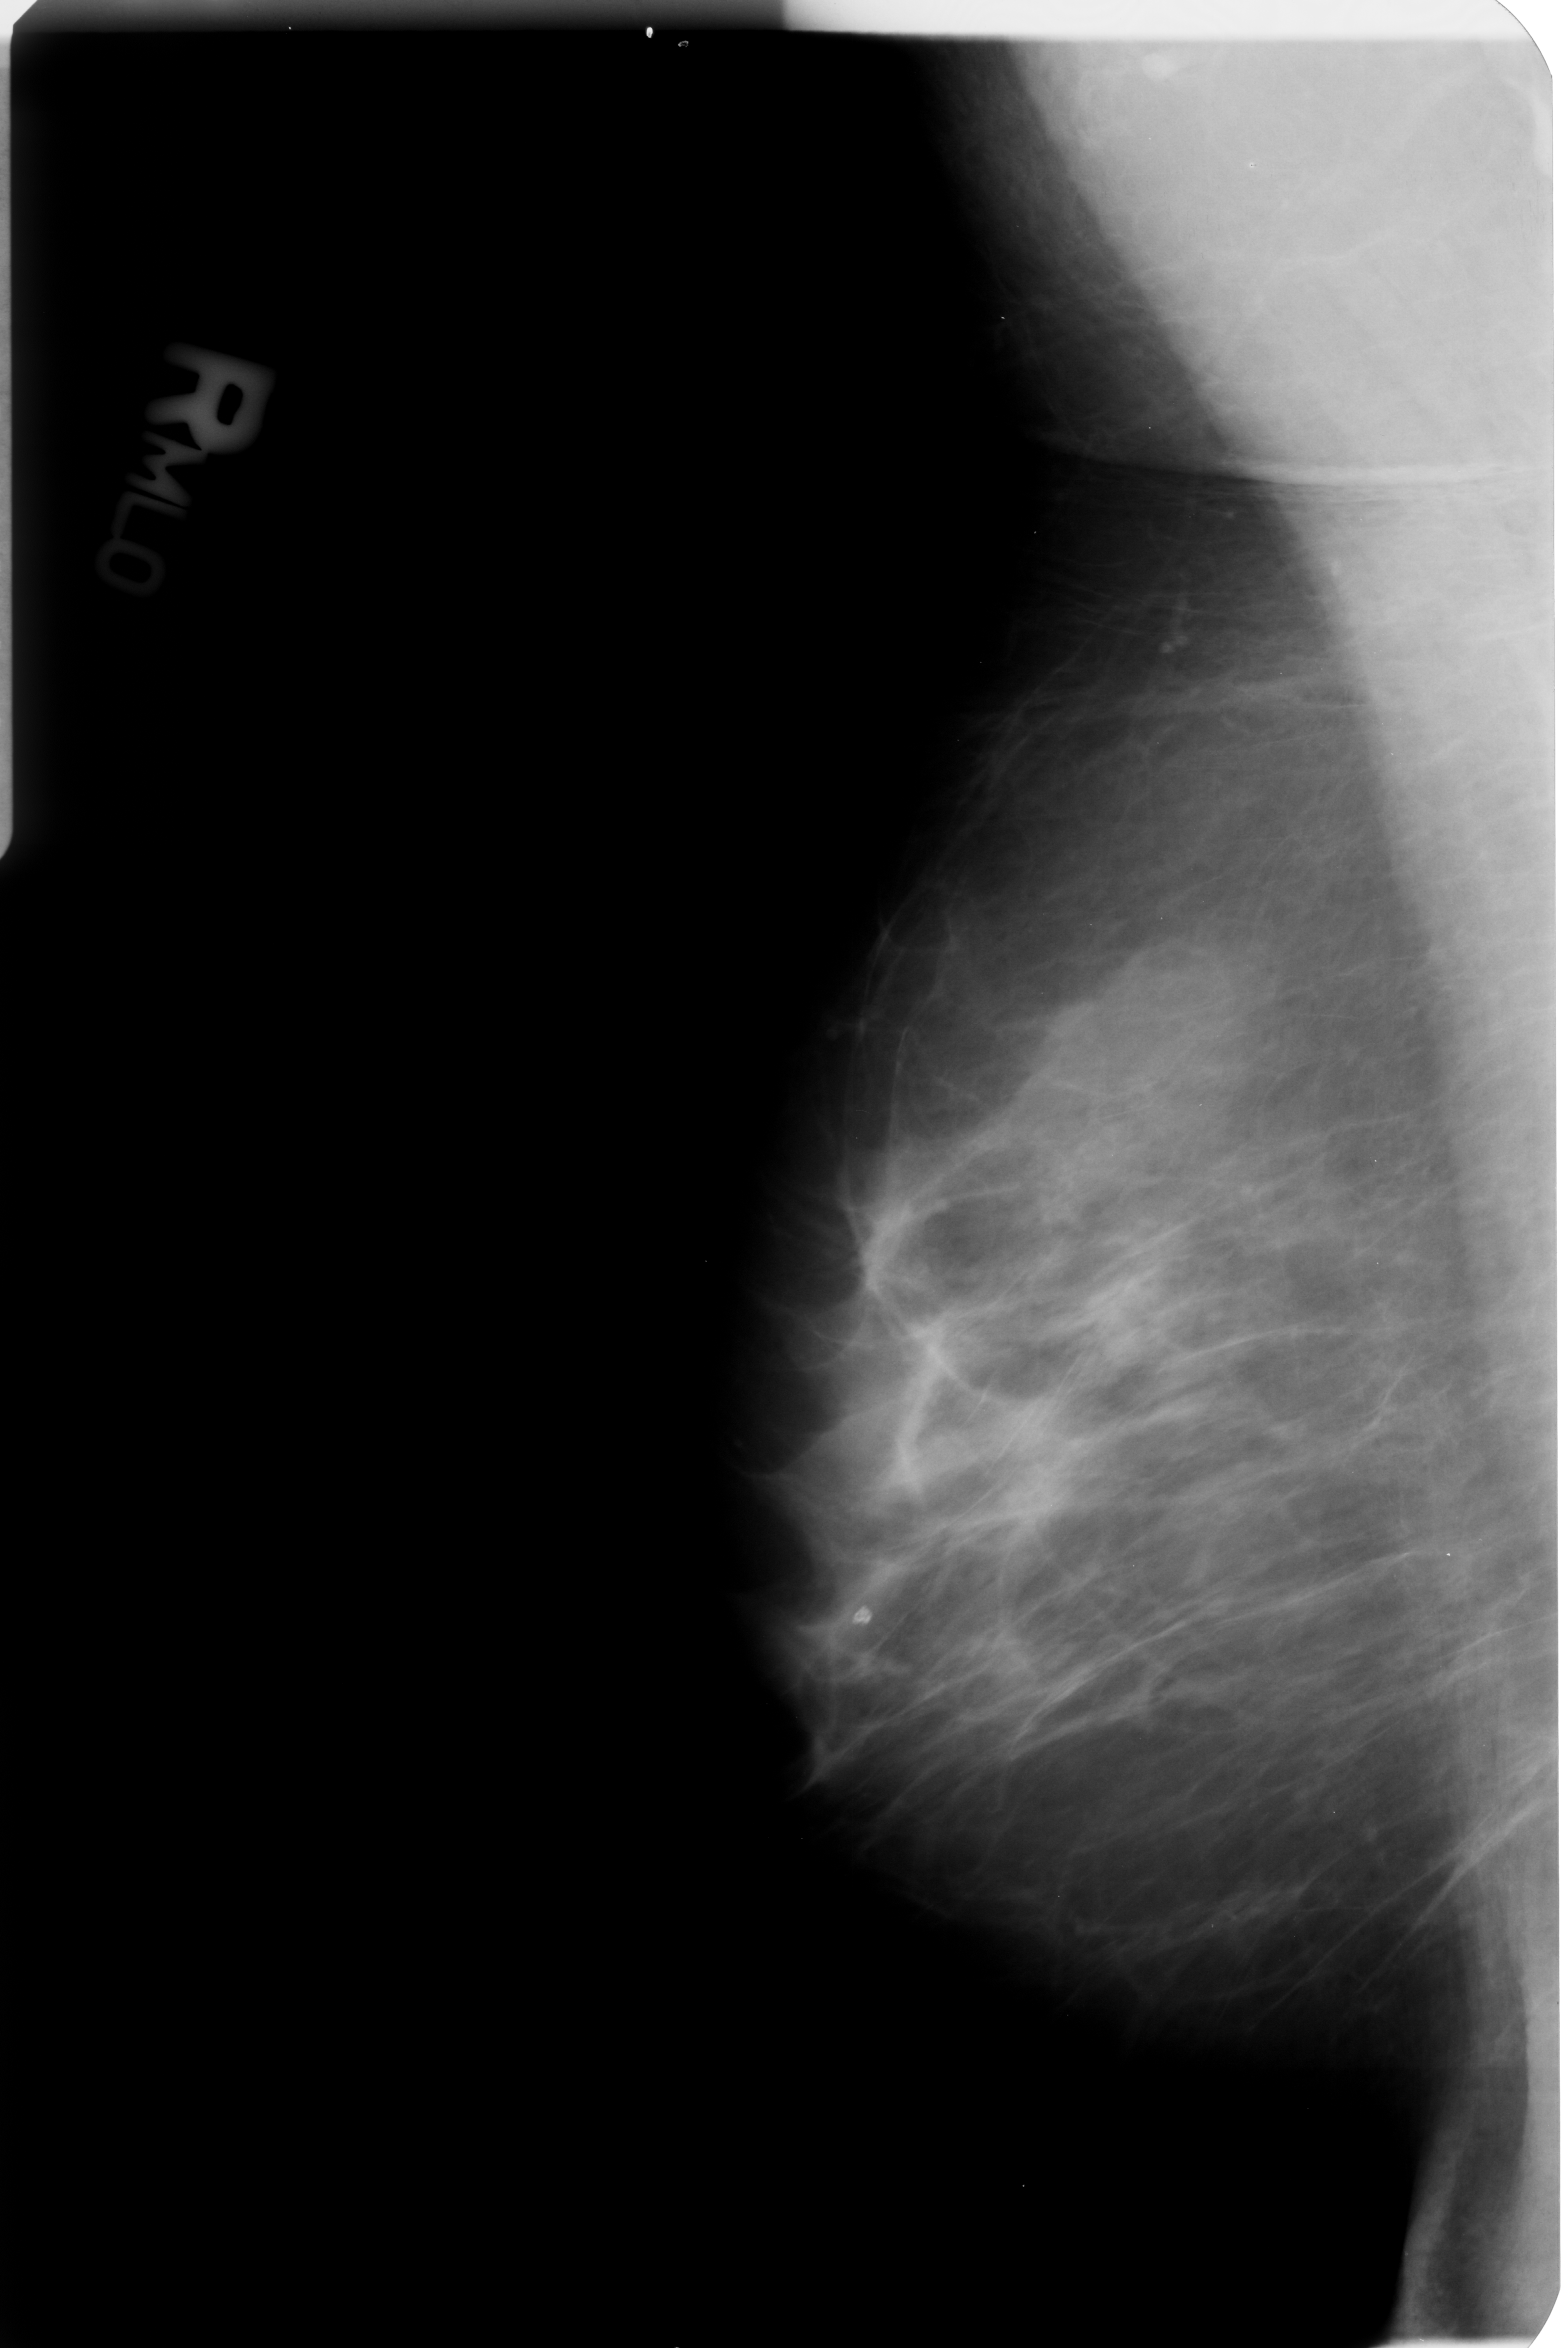
Digitized screen-film mammogram; right breast; MLO view; BI-RADS breast density category 2 (scale 1–4).
Marked abnormality: calcifications, morphology lucent center; BI-RADS assessment category 2; subtlety rating 5 on a 1 (subtle) to 5 (obvious) scale; benign; no additional work-up was recommended (benign without callback).